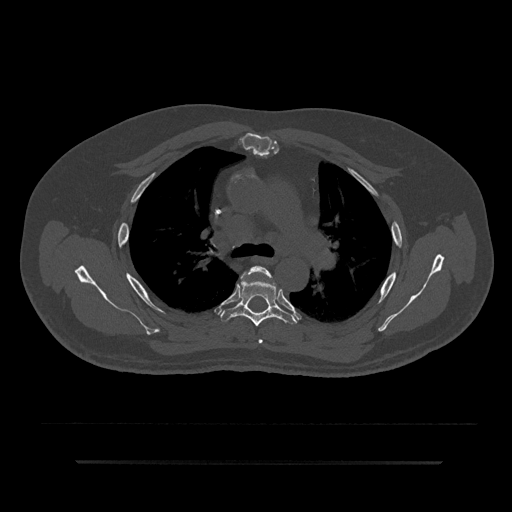
CT including the spine, one axial slice; position 582 of 797 along the scan axis; reconstruction kernel Br40s/3; 120 kVp; bone window (W 1800 / L 400 HU); 512 × 512 image matrix, field of view 464 × 464 mm. Male patient, age 59 years. Case-level facts recorded for this patient, not image findings: primary cancer: bile ducts.
Outlined on this slice (semi-automatically segmented with operator editing):
- T4 vertebra: box from (x=247, y=265) to (x=275, y=344) px
- T5 vertebra: (x=220, y=280)–(x=297, y=327)